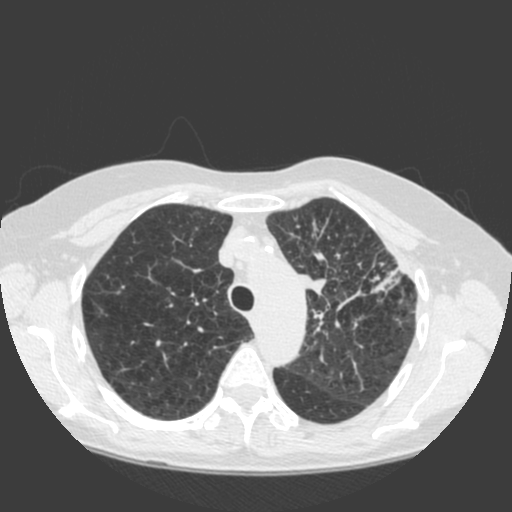
Low-dose screening chest CT, one axial slice. Position 144 of 184 along the scan axis. 120 kVp. Lung window (W 1500 / L -600 HU). 512 × 512 image matrix, field of view 350 × 350 mm.
Structures marked on this image (expert manual segmentation):
- lesion 1 (tumor, hilum of left lung): bounding box [x1, y1, x2, y2] px = [297, 273, 326, 295]